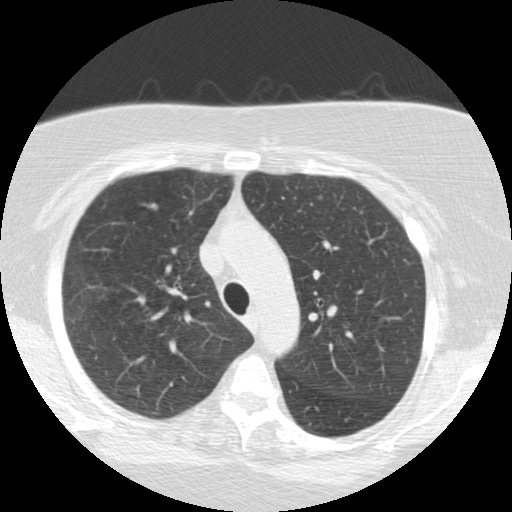
Low-dose screening chest CT, one axial slice. Slice 173 of 225 in the series (ordered by position). 120 kVp. Lung window (W 1500 / L -600 HU). 512 × 512 image matrix, field of view 320 × 320 mm.
Annotated regions visible in this slice (outlined manually by an expert reader):
- lesion 1 (tumor, upper lobe of right lung): box from (x=149, y=203) to (x=157, y=209) px